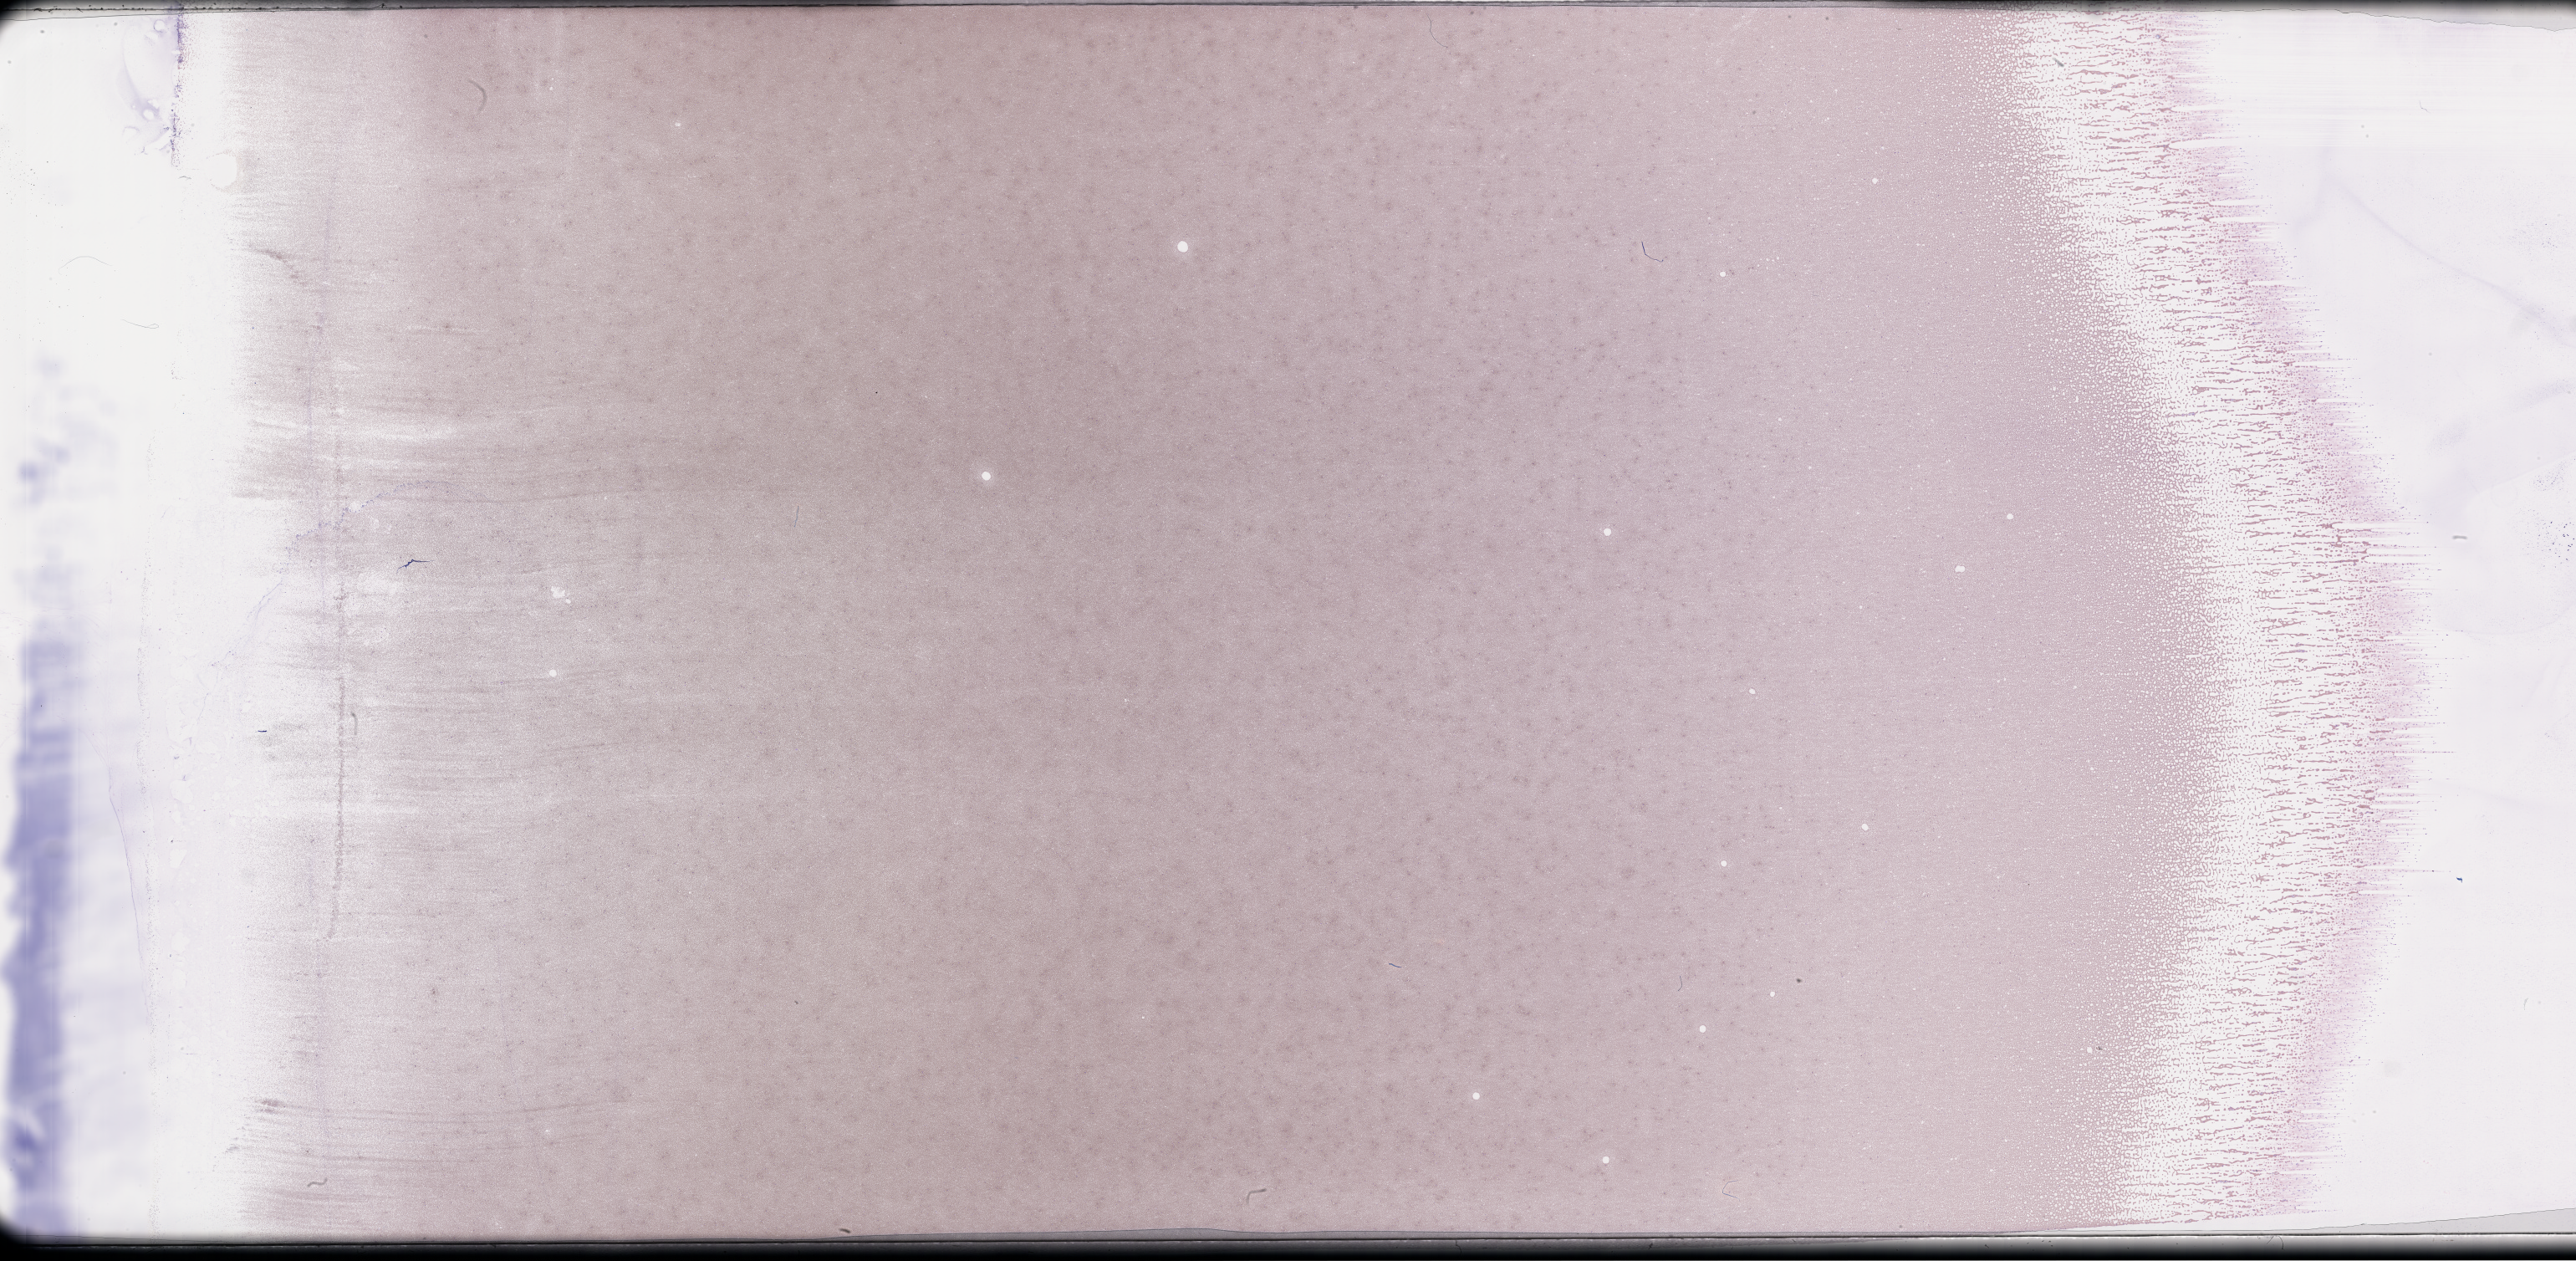
Wright–Giemsa-stained whole blood smear, whole-slide image, shown as a low-resolution overview of the whole scanned area (about 49.8 x 24.4 mm); smear from an EDTA sample; specimen time point: collected on treatment. Patient: male.
- patient diagnosis: Plasma Cell Myeloma